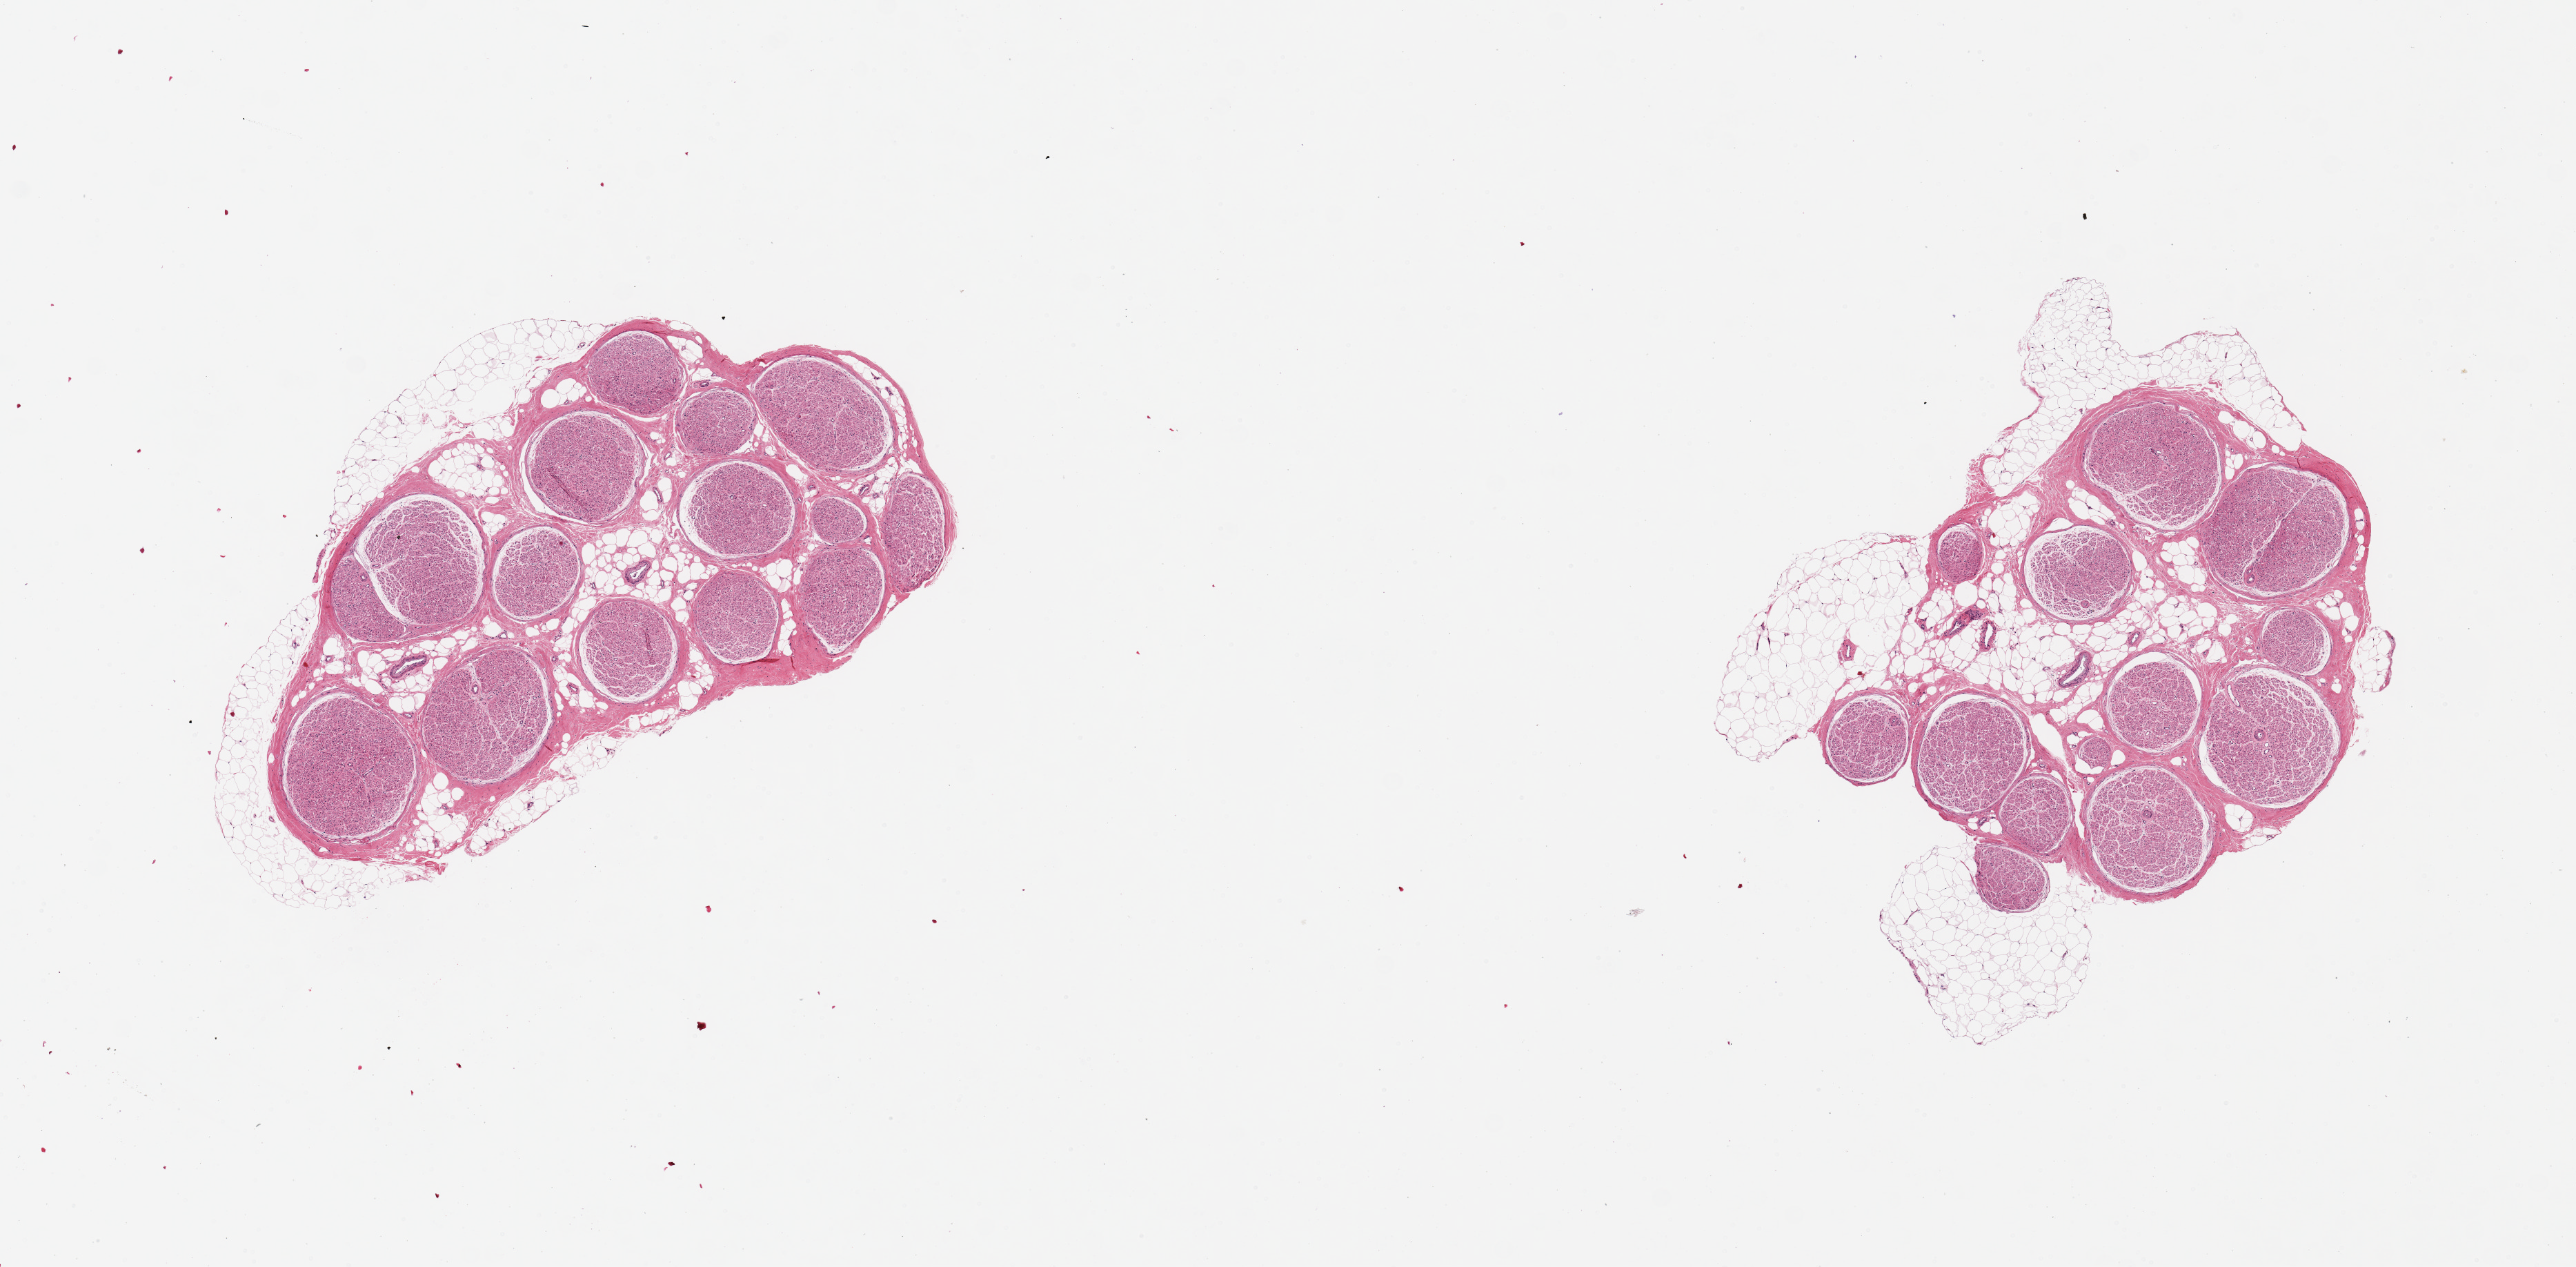
Digitized haematoxylin and eosin-stained section, low-resolution overview of the scanned area, about 14.8 x 7.3 mm. PAXgene-fixed paraffin-embedded (PFPE) section. Sampled site (target tissue): tibial nerve. Tissue donor sample.
- review note (as recorded): 2 pieces, 5x3 & 4x3mm; up to 40% adipose externally and internally among nerve fibers